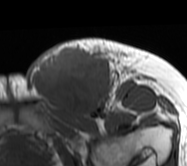
MRI of an extremity soft-tissue mass, one axial slice. Slice 33 of 62 in the series (ordered by position). MR volume resampled by the dataset authors to the PET/CT grid (not the native acquisition matrix). 3.27 mm slice thickness. 187 × 166 image matrix, field of view 183 × 162 mm. Female patient. Case-level facts recorded for this patient, not image findings: histological type: leiomyosarcoma; grade: high; site of the primary tumour: groin.
Annotated regions visible in this slice (expert contour drawn on MRI and transferred to this co-registered scan by the dataset authors):
- gross tumour volume including surrounding oedema: bounding box <27,37,147,120> (left, top, right, bottom; pixels)
- gross tumour volume (mass): <29,44,113,118>